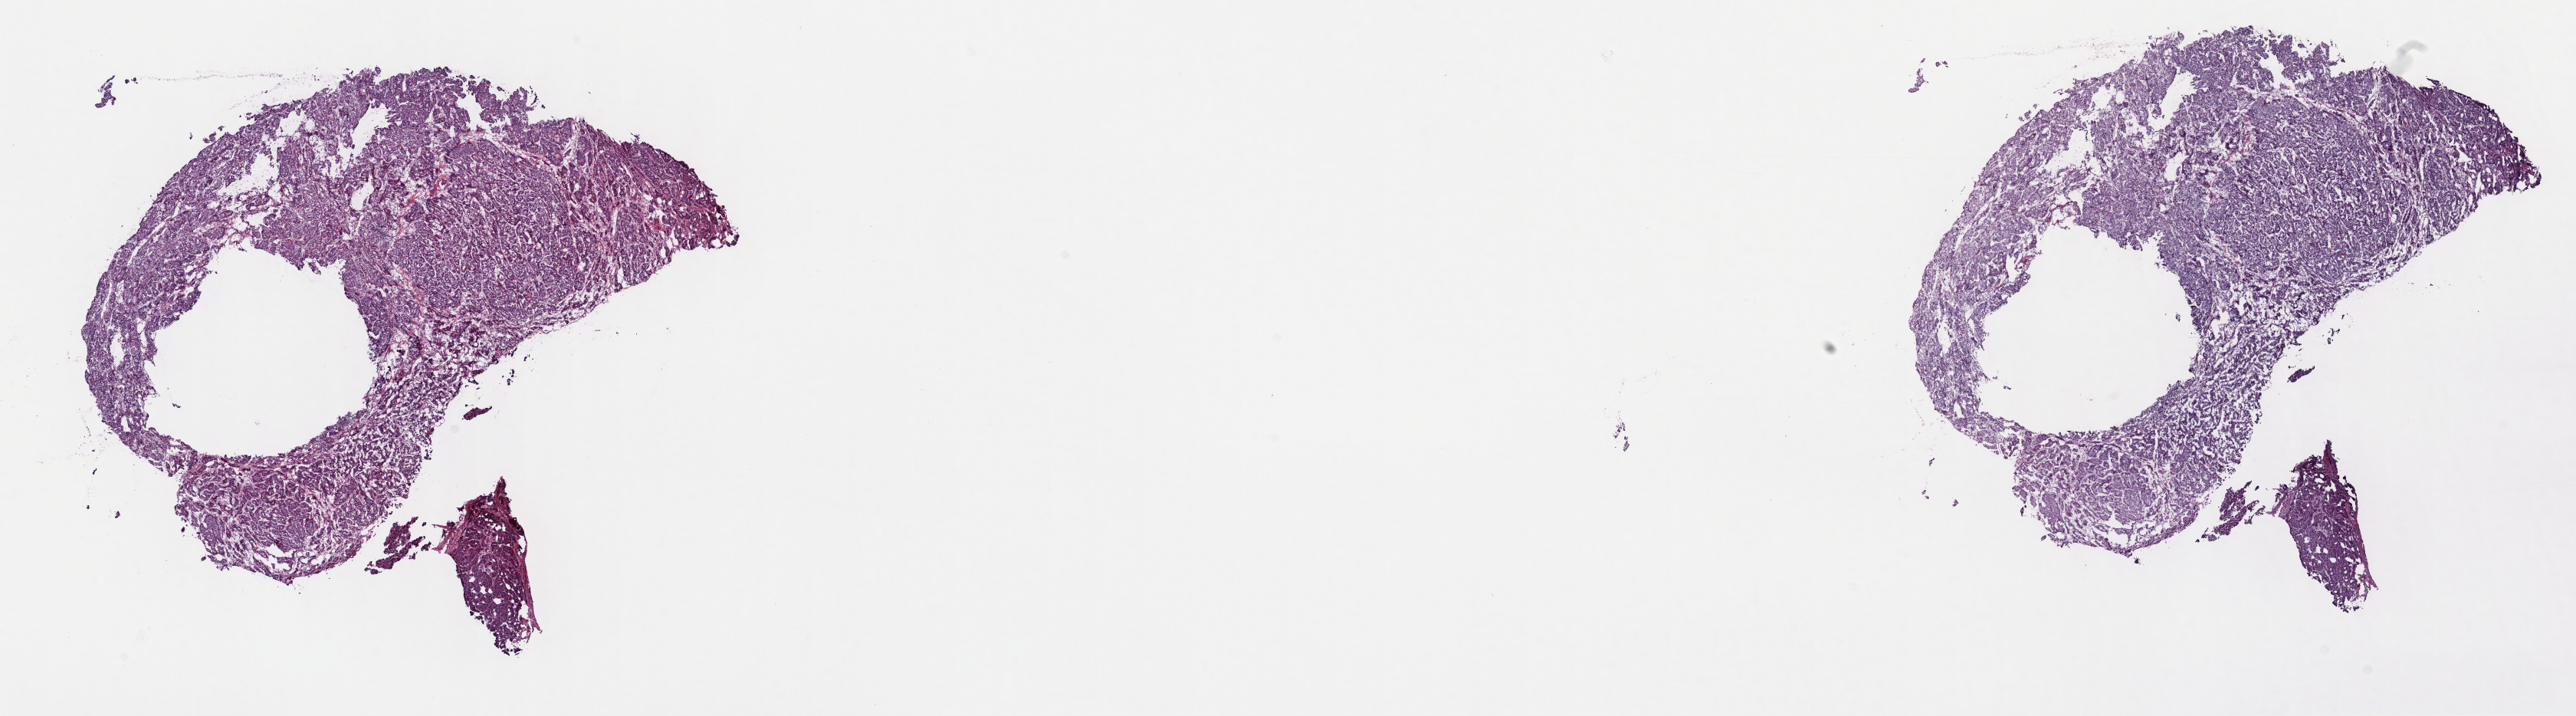
H&E-stained whole-slide image — low-resolution overview of the scanned area, about 27.2 x 7.6 mm, frozen section, liver, primary tumour sample. Male patient; age at initial diagnosis 56 years. Histologic grade: G2 (moderately differentiated). Pathologist review of this section (percent, as recorded): tumour cells 80%, tumour nuclei 80%, normal cells 0%, stromal cells 20%, necrosis 0%. Inflammatory infiltration, as recorded: lymphocyte infiltration 2%, monocyte infiltration 1%, neutrophil infiltration 3%.
AJCC pathologic stage: I (6th edition). Pathologic diagnosis: Hepatocellular carcinoma, NOS.